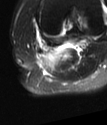
MRI of an extremity soft-tissue mass, one axial slice; position 53 of 78 along the scan axis; T2-weighted fat-saturated; MR volume resampled by the dataset authors to the PET/CT grid (not the native acquisition matrix); 107 × 125 image matrix, field of view 104 × 122 mm. Female patient. Case-level facts recorded for this patient, not image findings: histological type: extraskeletal high grade osteogenic sarcoma; grade: high; site of the primary tumour: left calf.
Annotated regions visible in this slice (expert contour drawn on MRI and transferred to this co-registered scan by the dataset authors):
- gross tumour volume (mass): bounding box <44,50,63,69> (left, top, right, bottom; pixels)